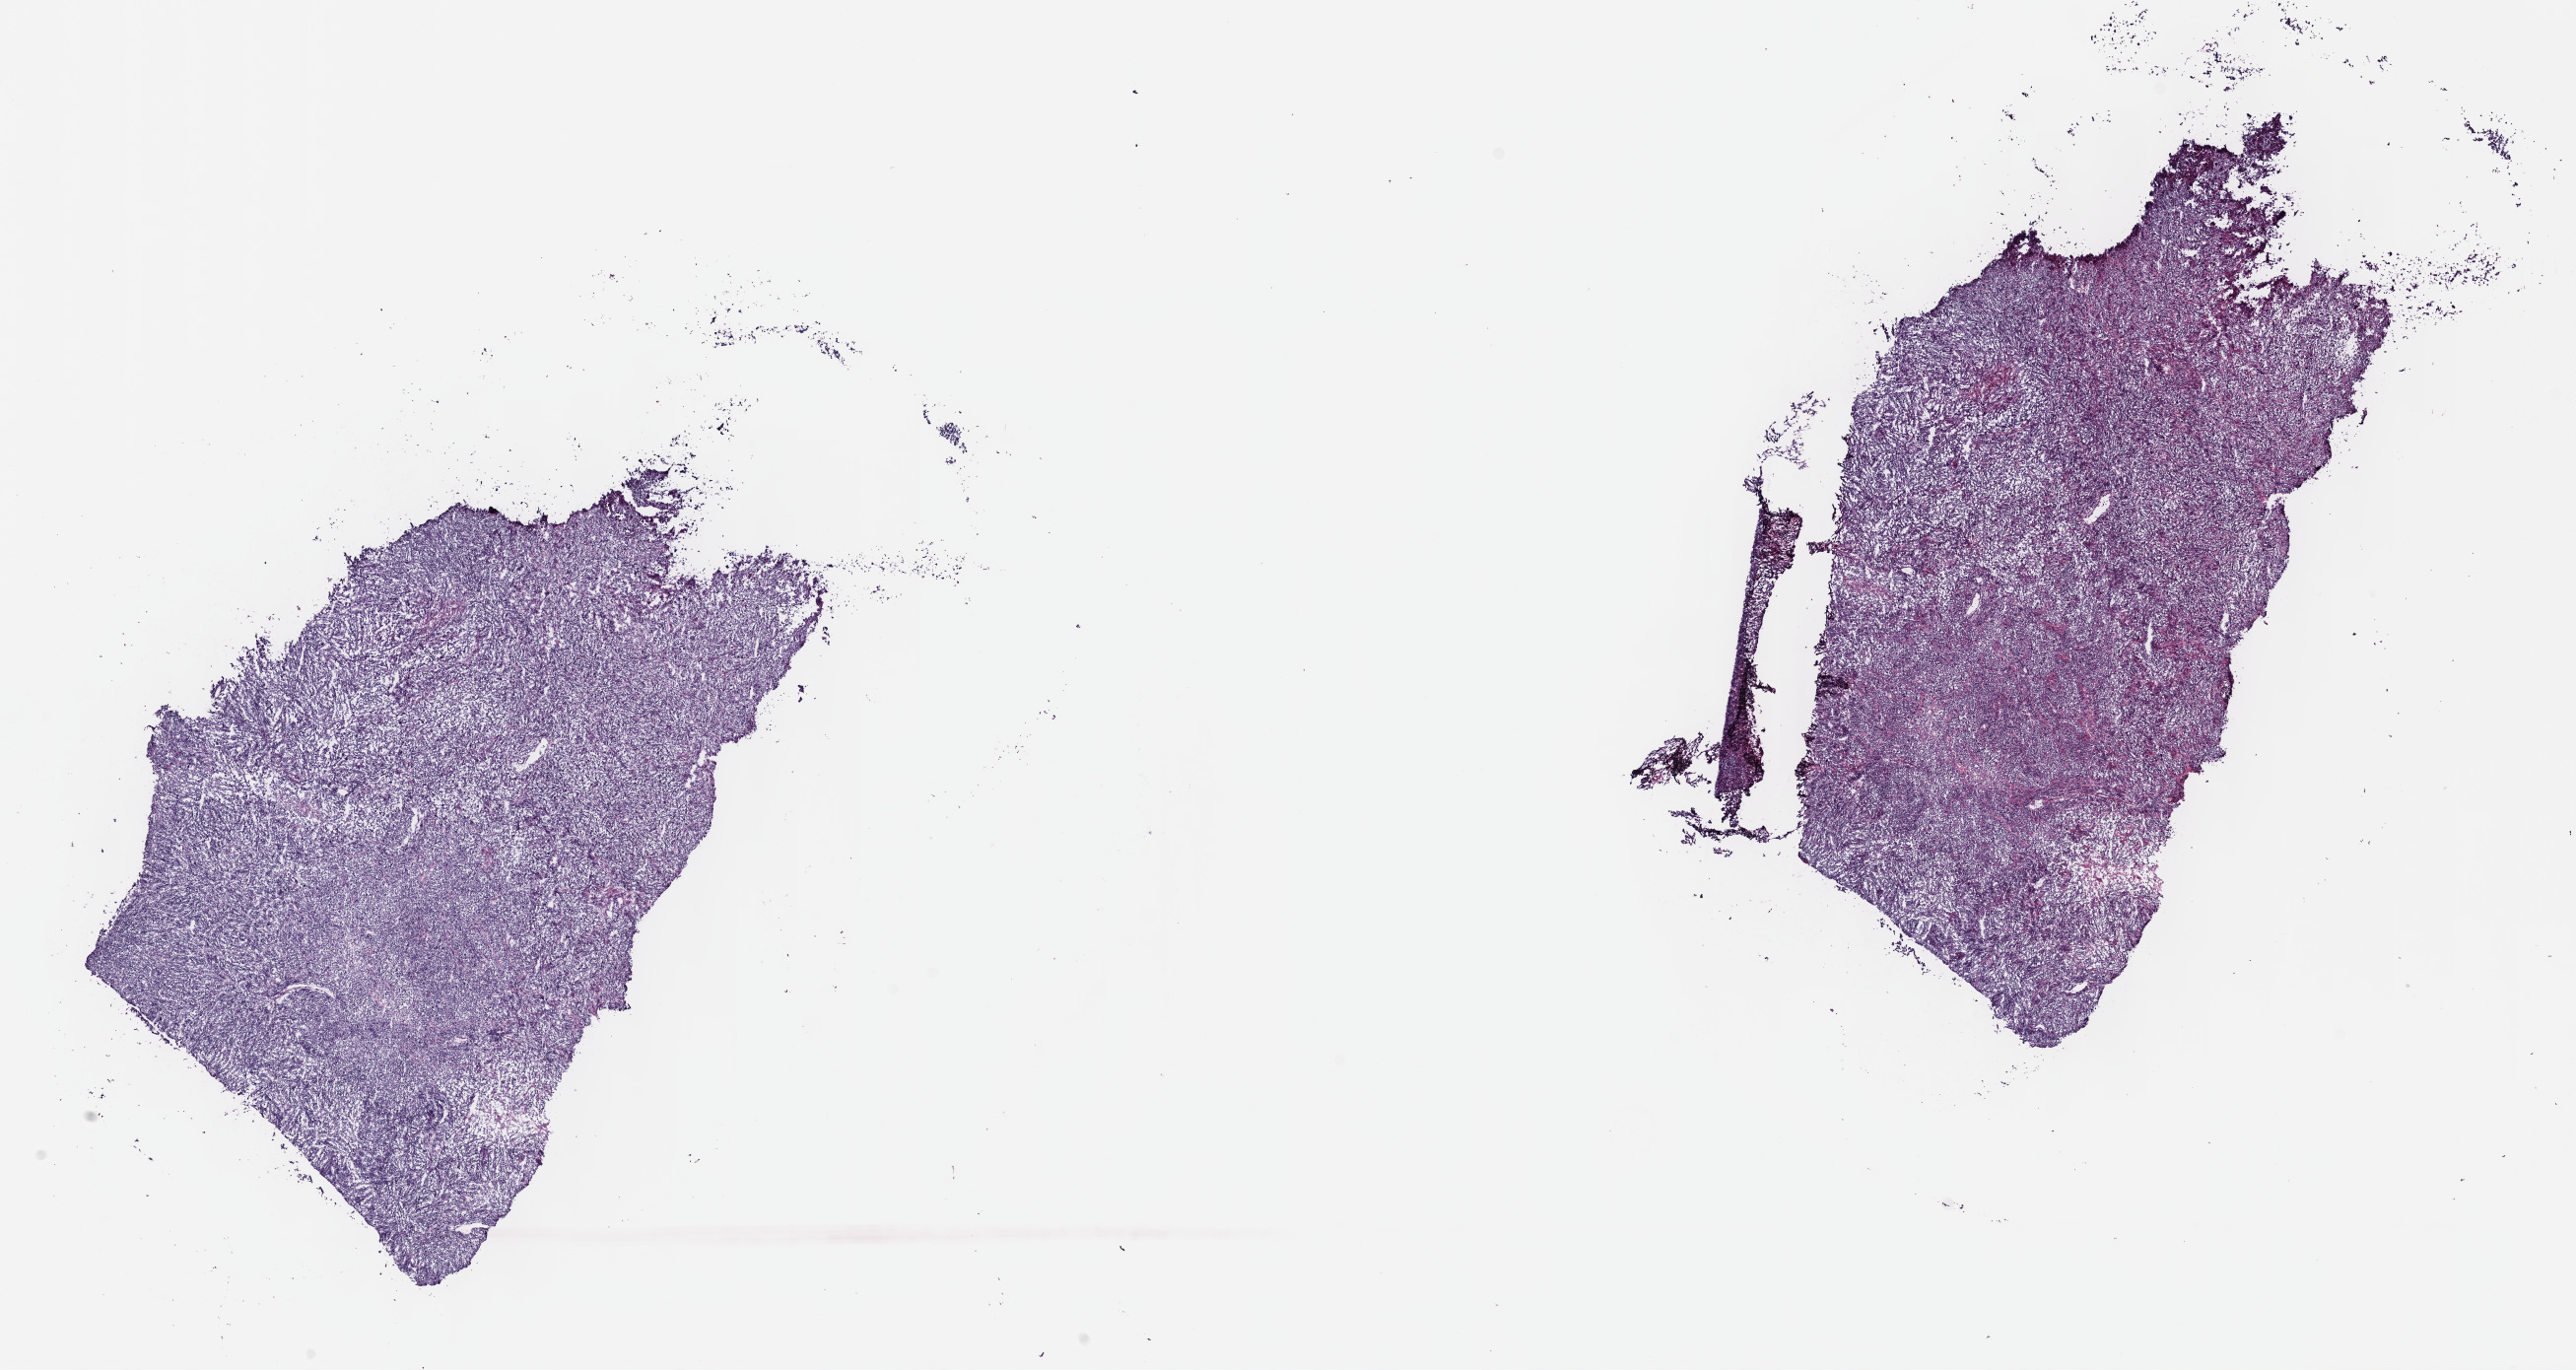
Whole-slide histology image, Hematoxylin and eosin (H&E) stained, shown as a low-resolution overview of the whole scanned area (about 21.1 x 11.2 mm), frozen section, metastatic tumour sample, sampled site: lymph nodes of axilla or arm. Female patient; age at initial diagnosis 65 years. Slide review estimates, as recorded: tumour cells 100%, tumour nuclei 80%, normal cells 0%, stromal cells 0%, necrosis 0%. Infiltration values recorded for this section: lymphocyte infiltration 2%, monocyte infiltration 0%, neutrophil infiltration 0%.
* this section: metastatic tumour tissue
* patient diagnosis: Malignant melanoma, NOS